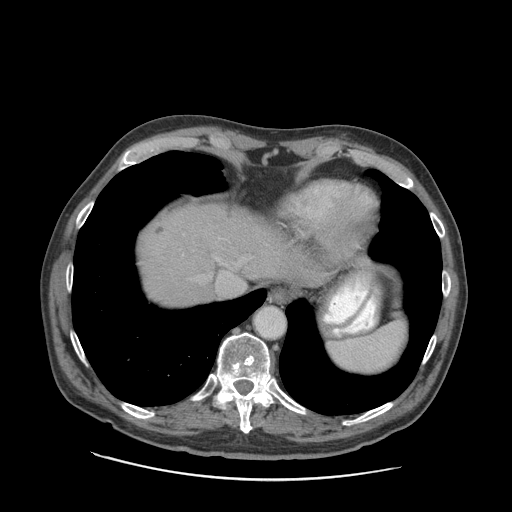
Contrast-enhanced abdominal CT (liver protocol), one axial slice. Position 77 of 89 along the scan axis. Reconstruction kernel STANDARD. 140 kVp. Soft-tissue window (W 400 / L 40 HU). 512 × 512 image matrix, field of view 420 × 420 mm. From the clinical record (not read from this slice): diagnosis: hepatocellular carcinoma (patient treated with transarterial chemoembolisation; whether this scan precedes or follows treatment is not stated here); TNM stage (as recorded): Stage-I; Child-Pugh class: A; tumour differentiation: moderately differentiated; tumour nodularity: uninodular.
Annotated regions visible in this slice (semi-automatic segmentation, software-assisted and operator-edited):
- liver parenchyma outside the tumour (the mass and vessels are separate outlines, so this box may not span the whole liver): bounding box [x1, y1, x2, y2] px = [140, 204, 328, 306]
- liver vessels: [216, 258, 230, 278]